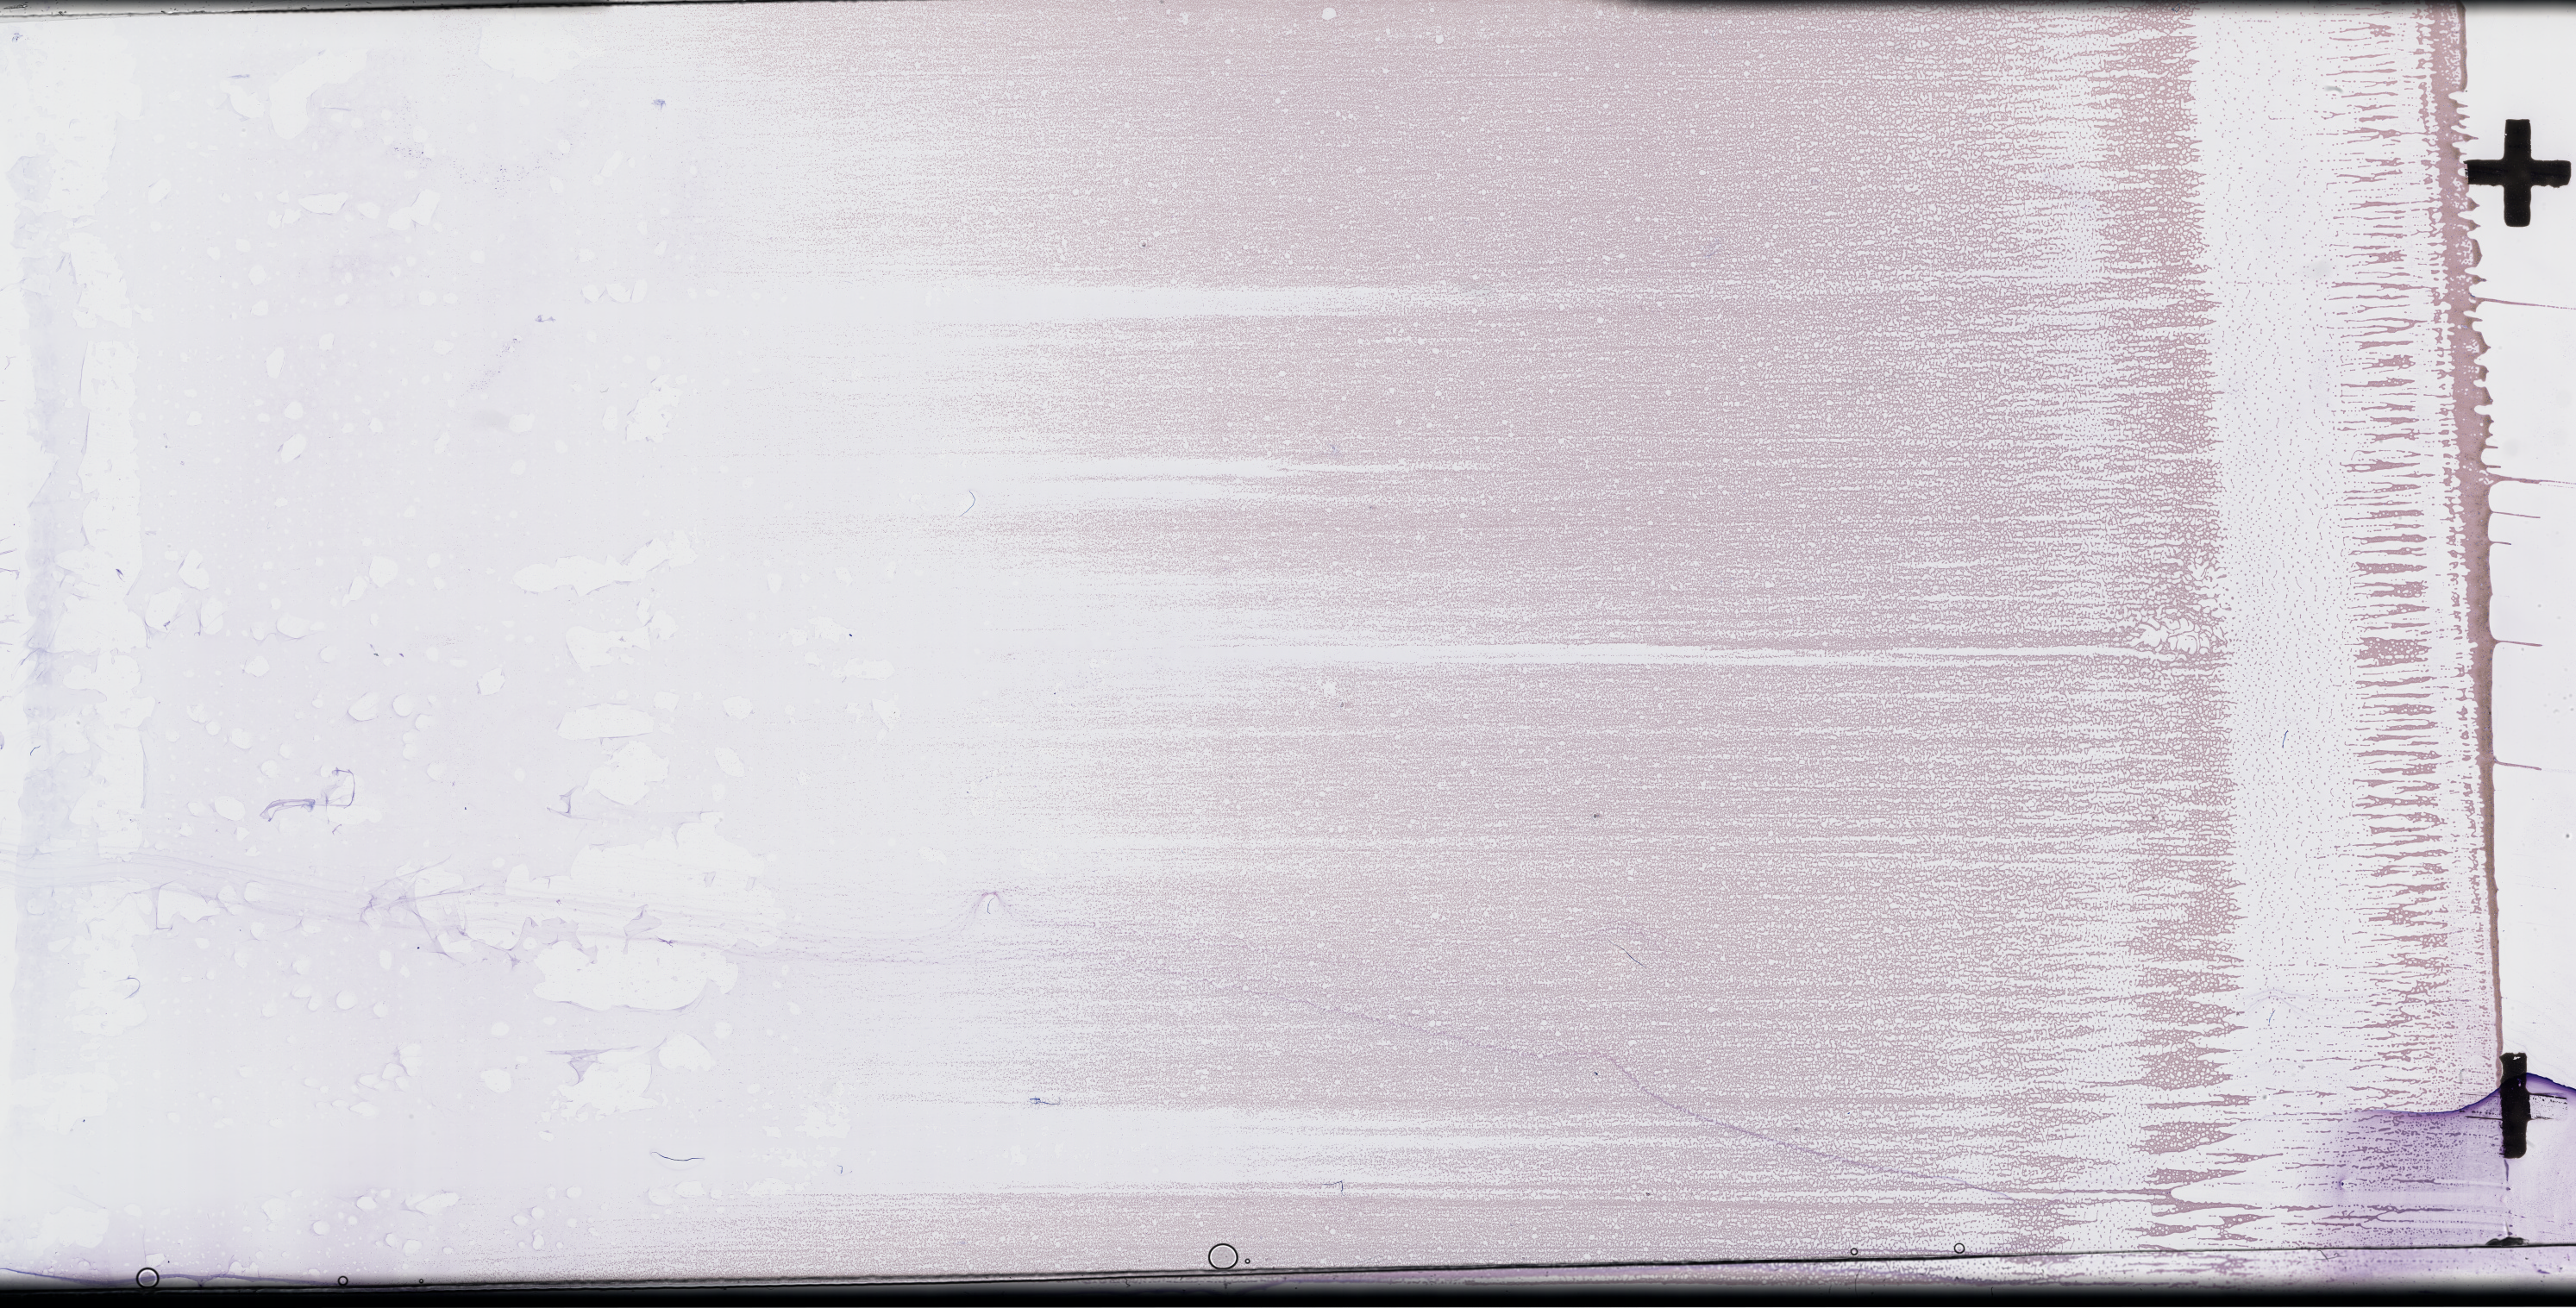
Wright–Giemsa-stained whole blood smear, whole-slide image — low-resolution overview of the scanned area, about 48.2 x 24.5 mm. Collected on treatment. Male patient.
Patient diagnosis: Plasma Cell Myeloma.